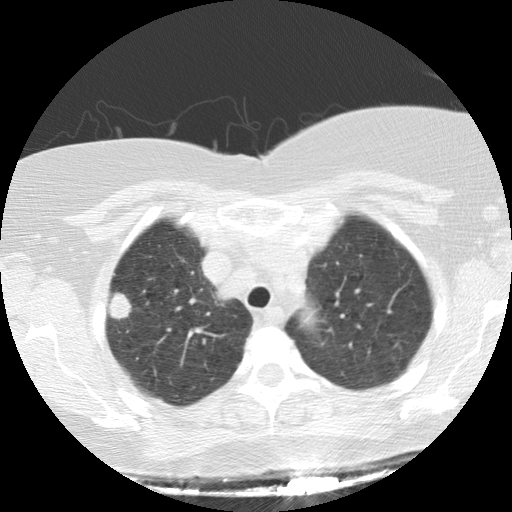
Axial slice from a low-dose chest CT screening exam. Baseline annual screen. Lung window (W 1500 / L -600 HU). 2.5 mm slice thickness. Standard (soft-tissue) reconstruction kernel (STANDARD). 512 × 512 image matrix. Female, age 64 years at enrolment. Current smoker at enrolment.
- Expert-annotated lung lesion, bounding box (x1, y1, x2, y2) in pixels: (94, 276, 144, 332).
- Reader record for this screening exam (exam-level; its link to the box is not recorded): non-calcified nodule or mass ≥4 mm, right upper lobe, 17 × 16 mm, spiculated (stellate) margins, soft tissue attenuation.
- Official screen result: positive, change unspecified: nodule(s) >= 4 mm or enlarging nodule(s), mass(es), or other non-specific abnormalities suspicious for lung cancer.
- Participant outcome: lung cancer diagnosed 70 days after this screen — adenocarcinoma, NOS, right upper lobe, stage IIIA (AJCC 6th edition), 15 mm at pathology.